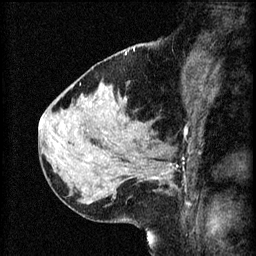
Breast MRI (dynamic contrast-enhanced), one sagittal slice; slice 26 of 60 in the series (ordered by position); 3 images stored at this slice position (order not interpretable as contrast timing); 1.5 T; TE 4.2 ms, TR 8.2 ms; 2 mm slice thickness; 256 × 256 image matrix. Female patient, age 37 years.
Structures marked on this image (semi-automatic segmentation, software-assisted and operator-edited):
- analysis volume of interest (the breast-tissue region the enhancement analysis was run in; not a lesion): bounding box <124,138,190,193> (left, top, right, bottom; pixels)
- tumour enhancement mask (voxels above the 70 % enhancement threshold inside the analysis volume of interest): <152,170,171,179>